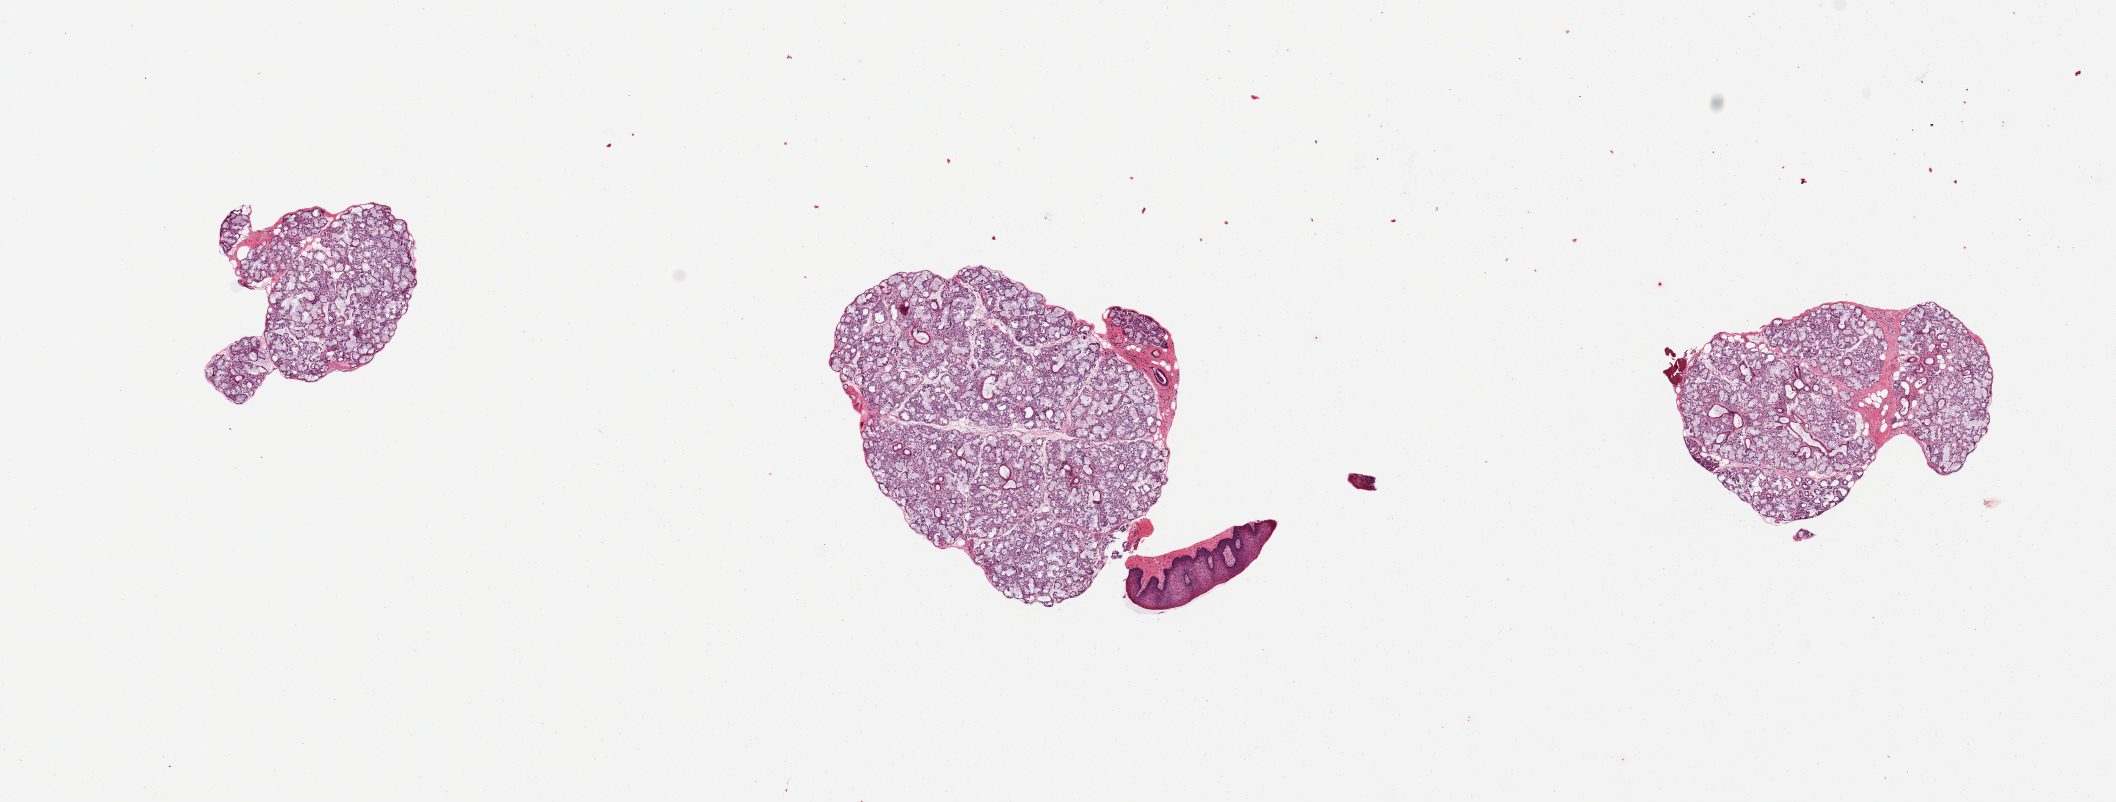
Whole-slide image, hematoxylin and eosin (H&E) stain — shown as a low-resolution overview of the whole scanned area (about 16.7 x 6.3 mm). PAXgene-fixed paraffin-embedded (PFPE) section. Section of minor salivary gland (target tissue). Donor tissue sample. Female donor.
• pathologist's review note for this sample: 3 pieces, excellent specimen, small detached fragment of squamous mucosa